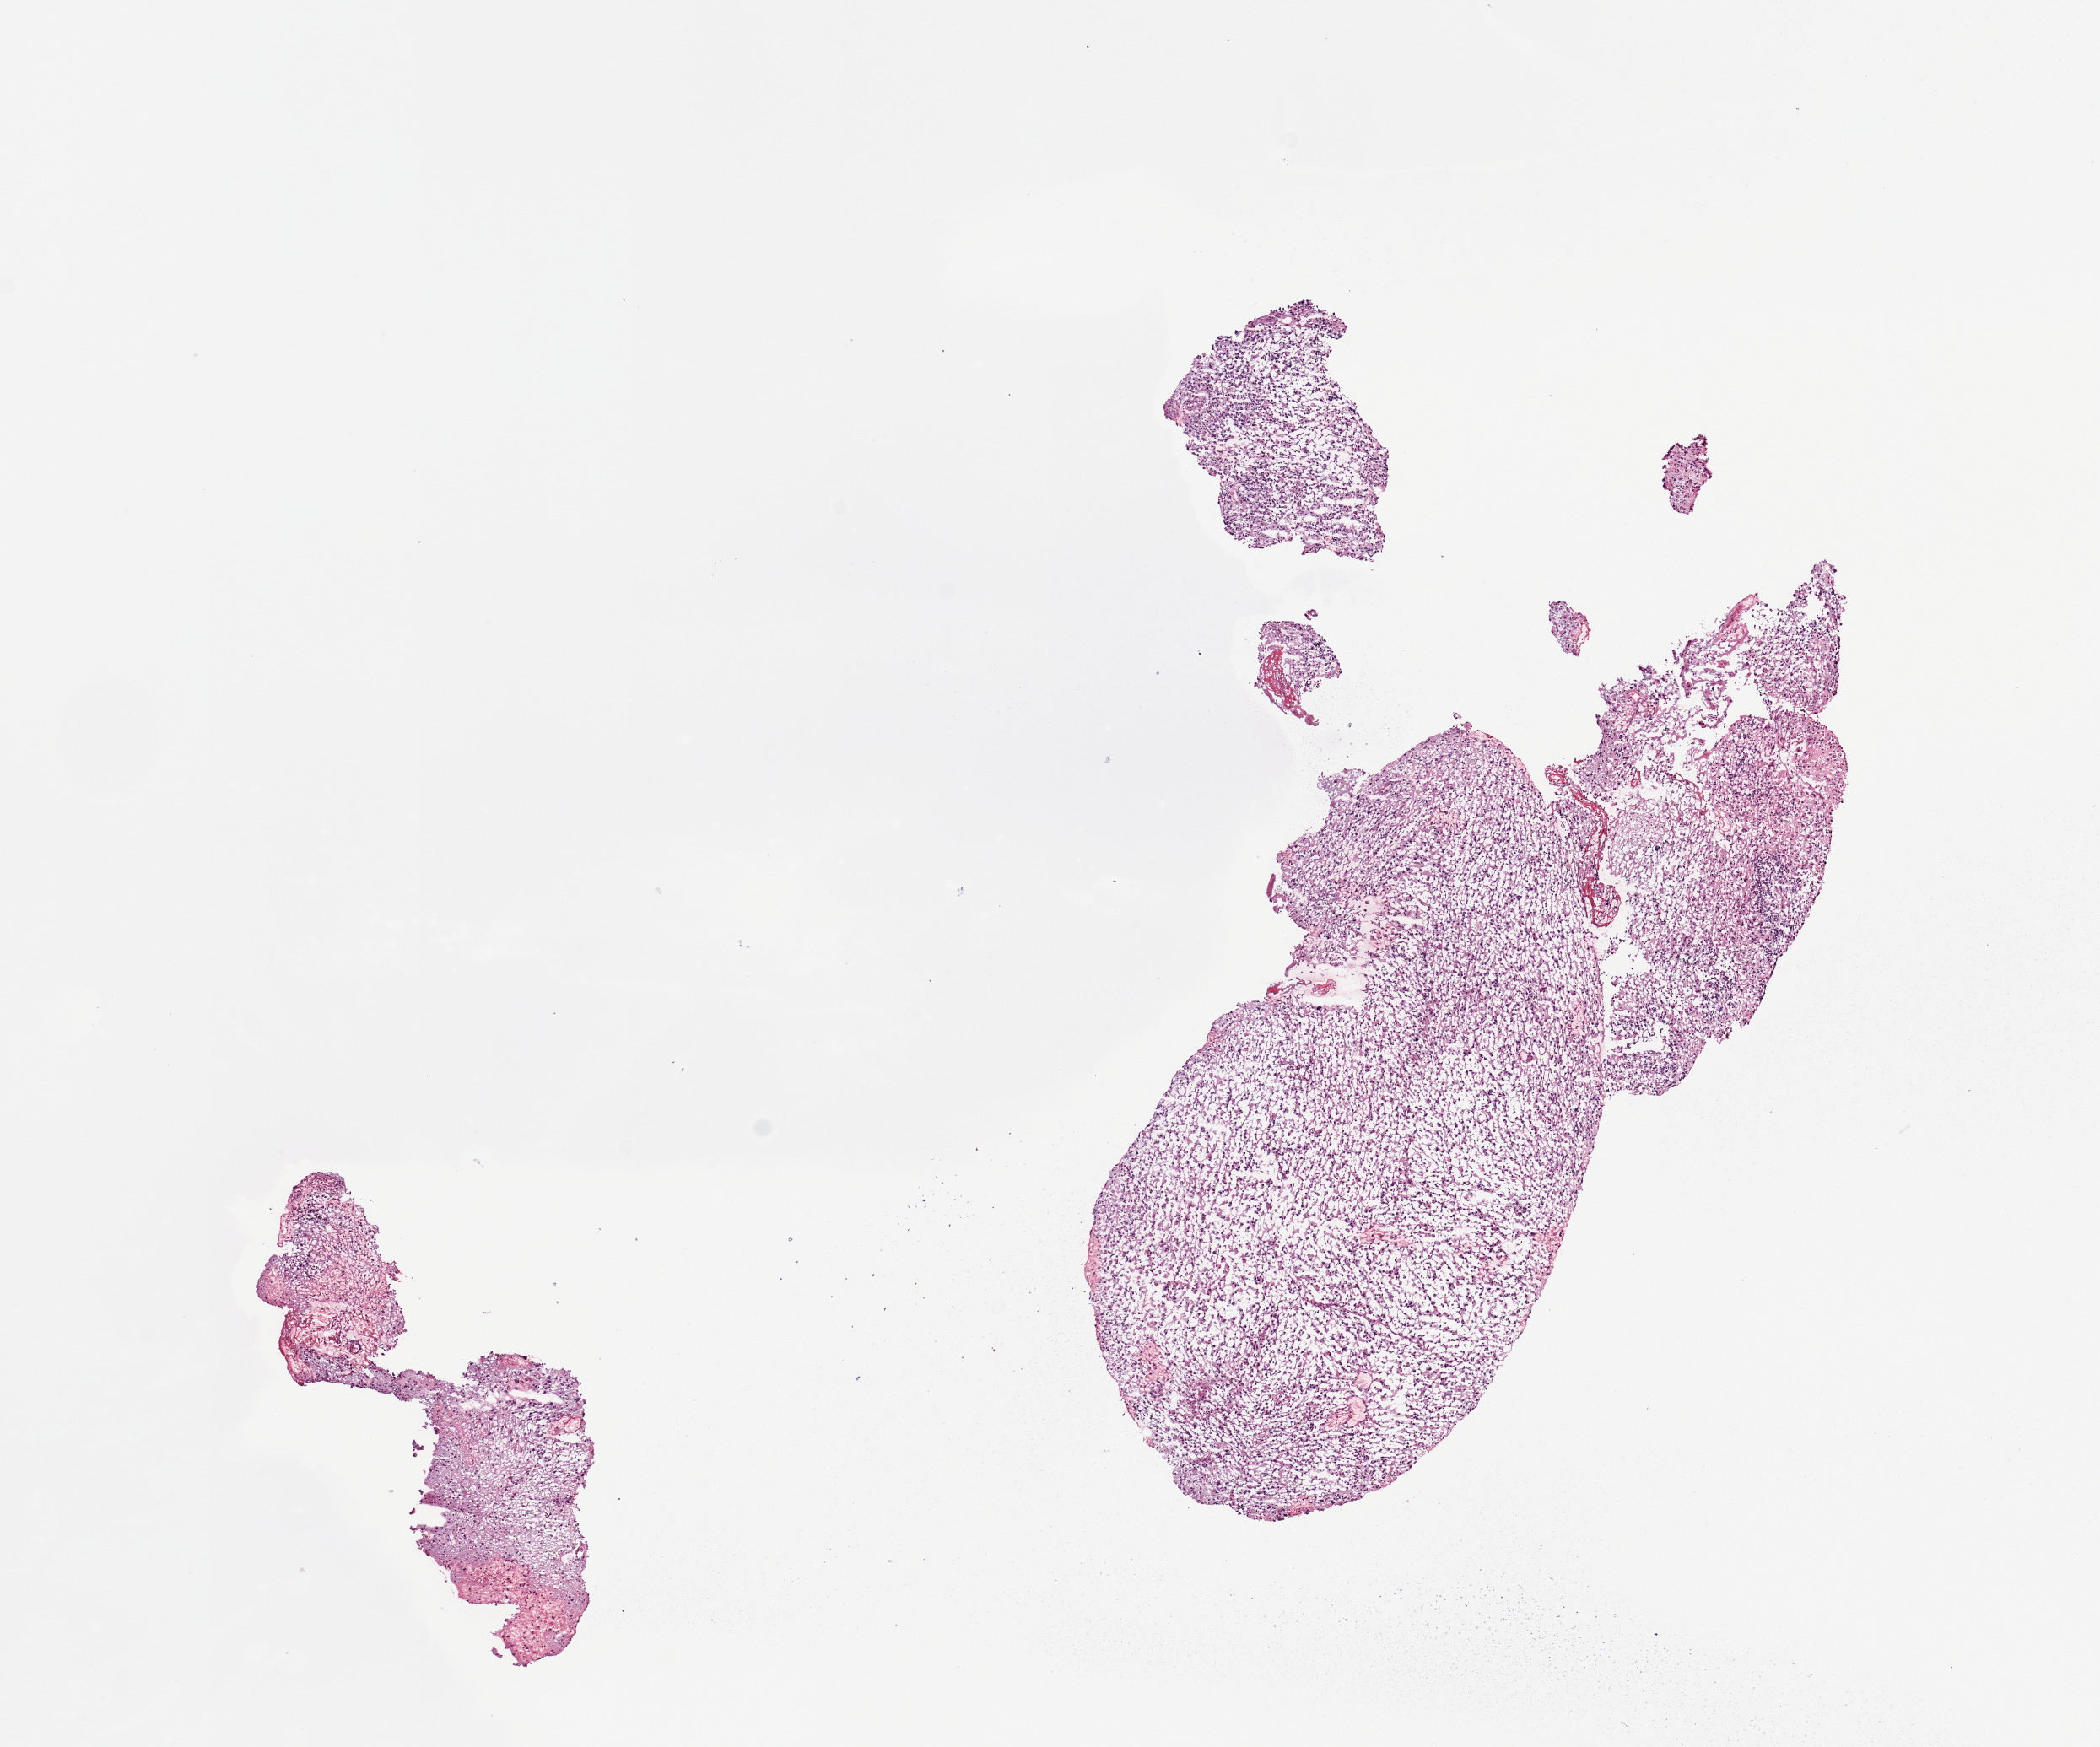
Digitized H&E-stained tissue section (whole slide), a low-resolution overview of the entire scanned area, about 9.8 x 8.2 mm; tumour tissue sample, brain. Patient: male, age 68 years.
Primary tumour site (as recorded): occipital lobe. Patient diagnosis (cohort enrolment): glioblastoma multiforme (brain).